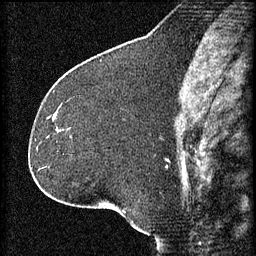
Breast MRI (dynamic contrast-enhanced), one sagittal slice. Position 29 of 60 along the scan axis. 3 images stored at this slice position (order not interpretable as contrast timing). 1.5 T. TE 4.2 ms, TR 8.2 ms. 2 mm slice thickness. 256 × 256 image matrix, field of view 180 × 180 mm. Patient: female, 32 years.
Outlined on this slice (semi-automatically segmented with operator editing):
- analysis volume of interest (the breast-tissue region the enhancement analysis was run in; not a lesion): bounding box <48,114,74,137> (left, top, right, bottom; pixels)
- tumour enhancement mask (voxels above the 70 % enhancement threshold inside the analysis volume of interest): <54,116,56,119>